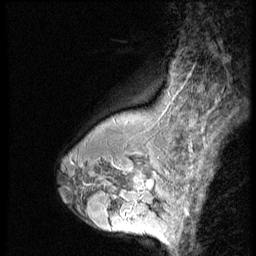
Breast MRI (dynamic contrast-enhanced), one sagittal slice. Position 41 of 56 along the scan axis. 3 images stored at this slice position (order not interpretable as contrast timing). 1.5 T. TE 4.2 ms, TR 9 ms. 2.5 mm slice thickness. 256 × 256 image matrix, field of view 180 × 180 mm. Patient: female, 43 years. From the clinical record (not read from this slice): setting: breast cancer imaged before/during neoadjuvant chemotherapy; receptor status: HR-positive, HER2-negative.
Annotated regions visible in this slice (semi-automatically segmented with operator editing):
- analysis volume of interest (the breast-tissue region the enhancement analysis was run in; not a lesion): box from (x=120, y=160) to (x=163, y=207) px
- tumour enhancement mask (voxels above the 140 % enhancement threshold inside the analysis volume of interest): (x=133, y=176)–(x=155, y=189)